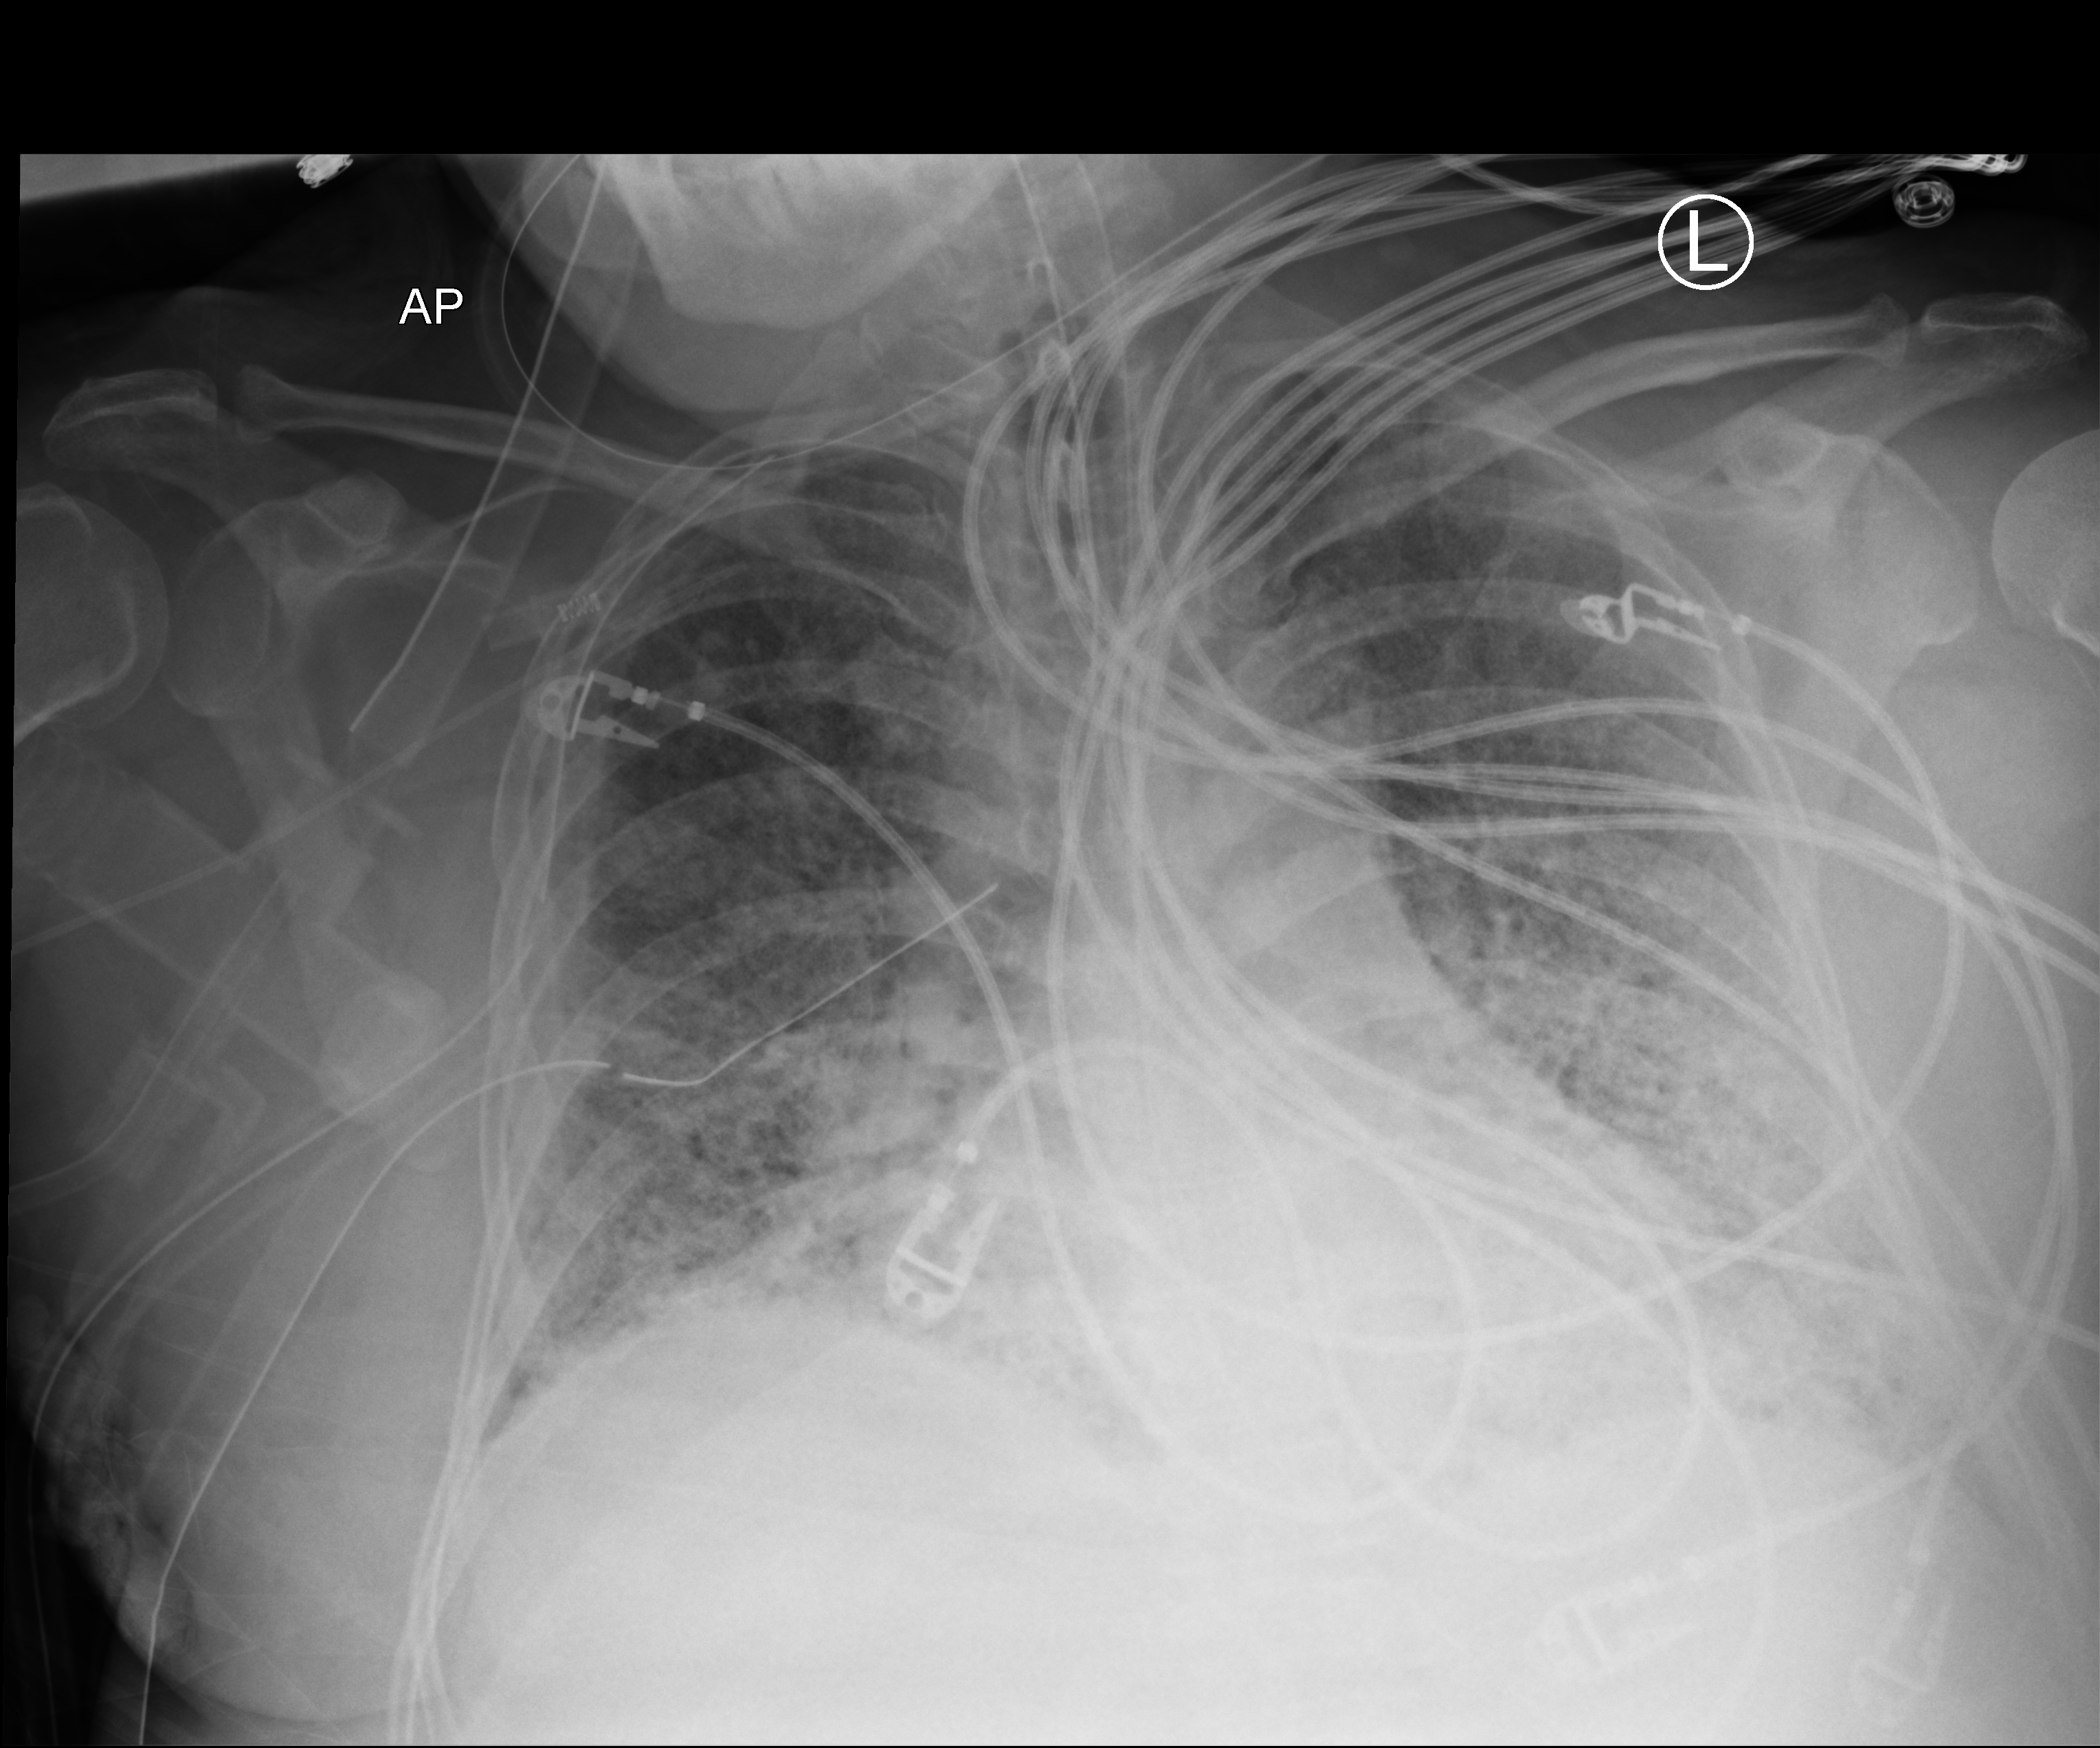
Bedside chest radiograph (computed radiography), anteroposterior (AP) projection. Adult patient hospitalised with COVID-19, age 18–59 years.
Admission-level facts for this patient (not findings on this image; timing relative to this image not recorded): smoking status (admission record): never; admitted to intensive care during this hospital stay: yes; mechanically ventilated during this hospital stay: yes.